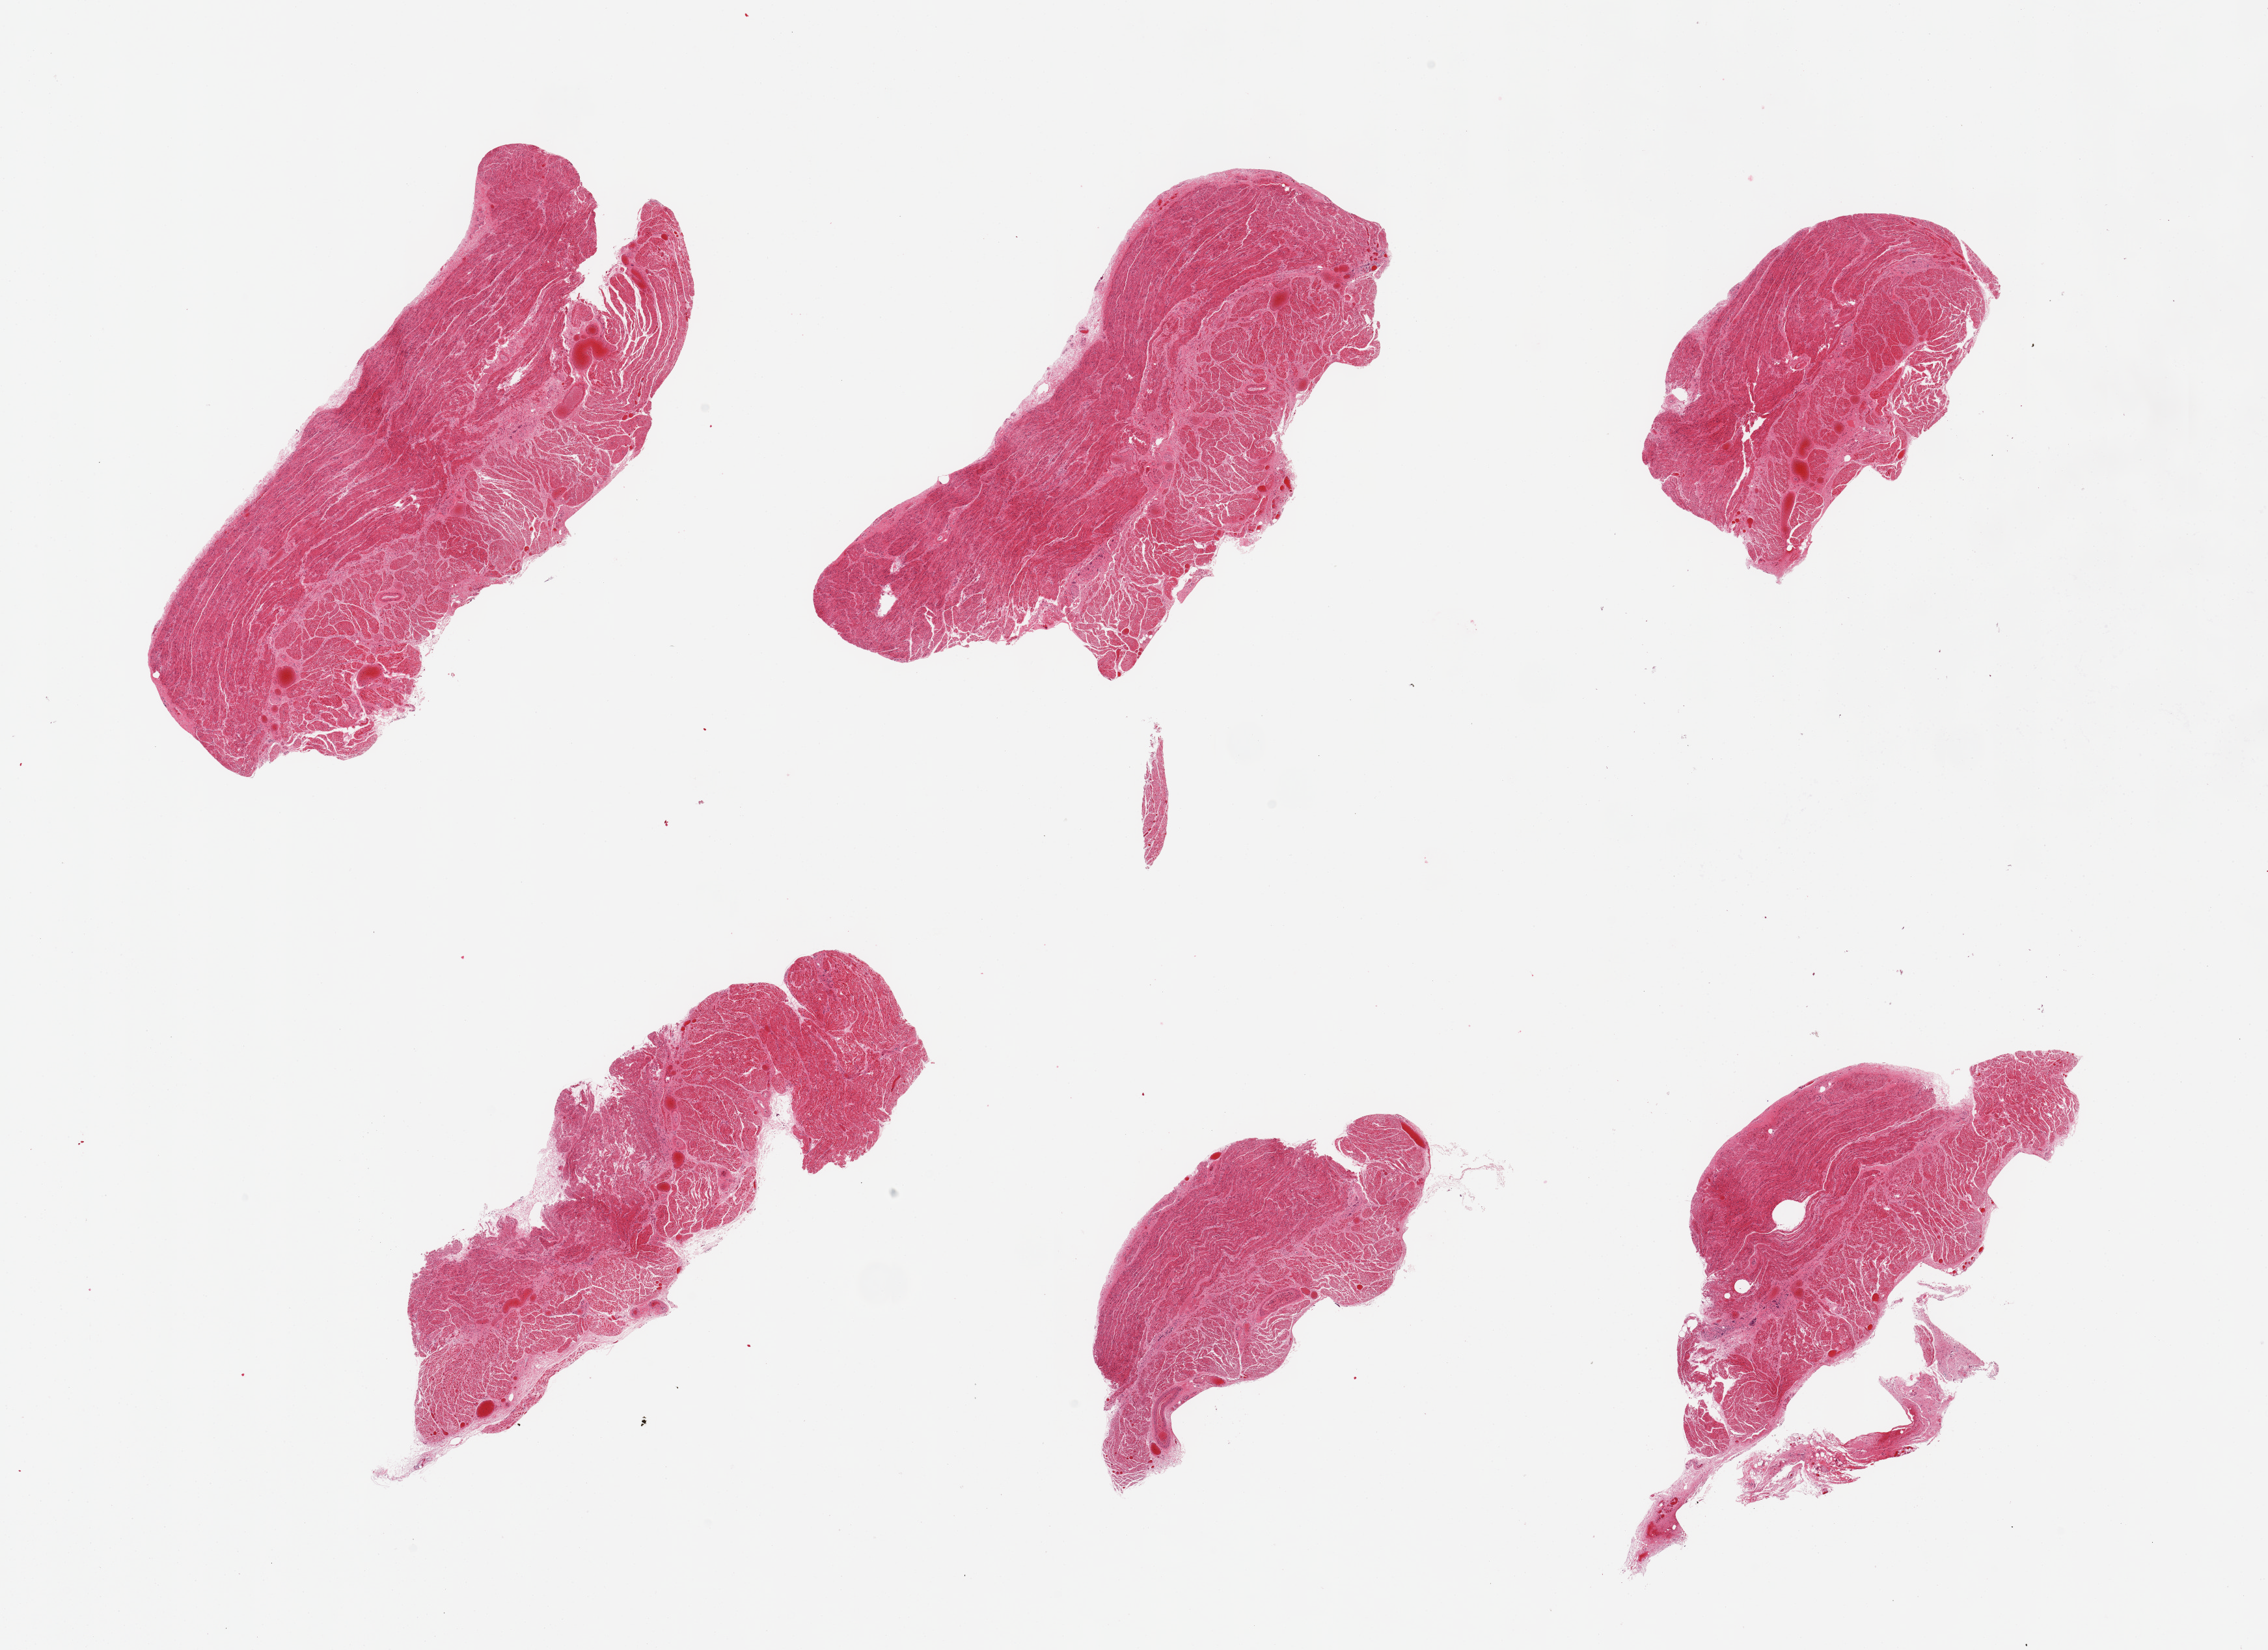
Whole-slide image, hematoxylin and eosin (H&E) stain, a low-resolution overview of the entire scanned area, about 27.6 x 20.1 mm; PAXgene-fixed paraffin-embedded (PFPE) section; target tissue: gastroesophageal junction; tissue donor sample.
Review note (as recorded): 6 pieces; well trimmed.